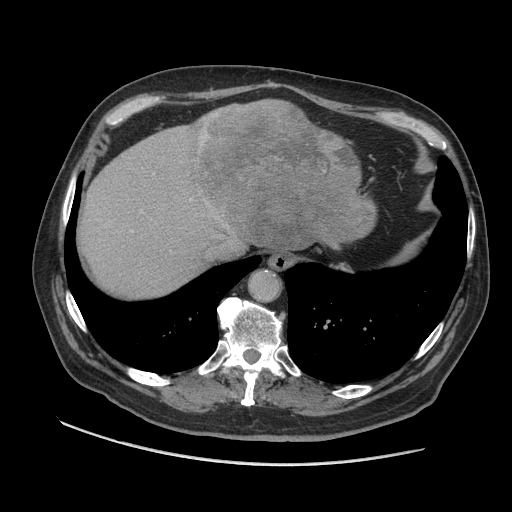
Contrast-enhanced abdominal CT (liver protocol), one axial slice. Position 81 of 109 along the scan axis. Reconstruction kernel STANDARD. Soft-tissue window (W 400 / L 40 HU). 512 × 512 image matrix, field of view 420 × 420 mm. From the clinical record (not read from this slice): diagnosis: hepatocellular carcinoma (patient treated with transarterial chemoembolisation; whether this scan precedes or follows treatment is not stated here); TNM stage (as recorded): Stage-I; Child-Pugh class: A; tumour nodularity: uninodular.
Structures marked on this image (semi-automatically segmented with operator editing):
- liver parenchyma outside the tumour (the mass and vessels are separate outlines, so this box may not span the whole liver): bounding box <78,100,360,296> (left, top, right, bottom; pixels)
- mass: <190,100,377,251>